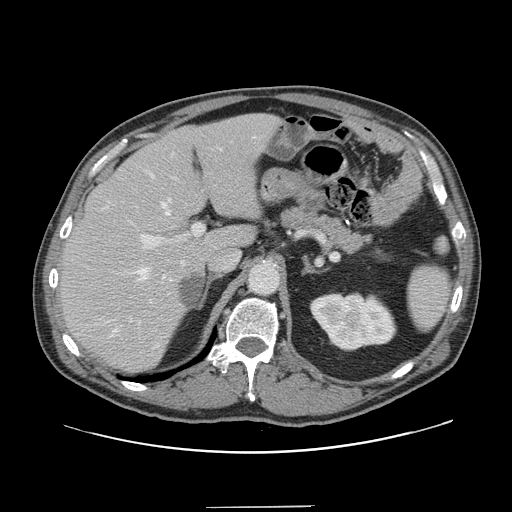
Contrast-enhanced abdominal CT, one axial slice; position 95 of 139 along the scan axis; intravenous contrast given; soft-tissue window (W 400 / L 40 HU); 2.5 mm slice thickness; 512 × 512 image matrix, field of view 397 × 397 mm. Male patient, age 64 years. Case-level facts recorded for this patient, not image findings: diagnosis: colorectal cancer liver metastases, imaged before liver resection; multiple liver metastases: yes; largest metastasis: 3.5 cm.
Structures marked on this image (expert manual segmentation):
- hepatic veins: bounding box <130,137,255,321> (left, top, right, bottom; pixels)
- liver: <62,115,276,370>
- planned liver remnant (the part of the liver to remain after resection): <62,115,270,370>
- portal vein (with intrahepatic branches): <138,223,205,324>
- liver metastasis: <178,273,202,309>